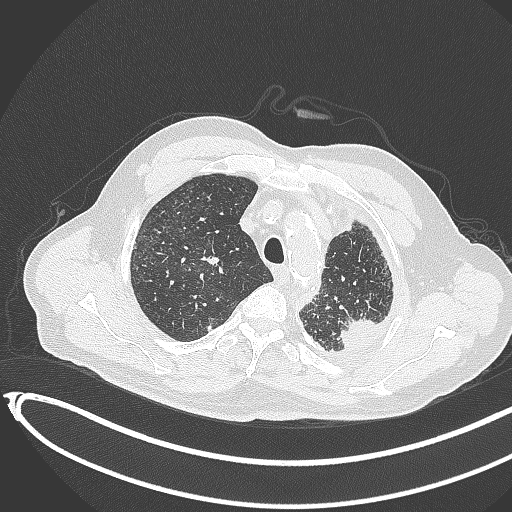
Chest CT, one axial slice. Slice 350 of 451 in the series (ordered by position). 120 kVp. Lung window (W 1500 / L -600 HU). 512 × 512 image matrix, field of view 400 × 400 mm. Male patient, age 78 years. Case-level facts recorded for this patient, not image findings: clinical TNM (as recorded): T1c N0 M1.
Outlined on this slice (bounding box drawn by a radiologist):
- lung tumour (recorded histology: adenocarcinoma): bounding box <337,311,380,357> (left, top, right, bottom; pixels)